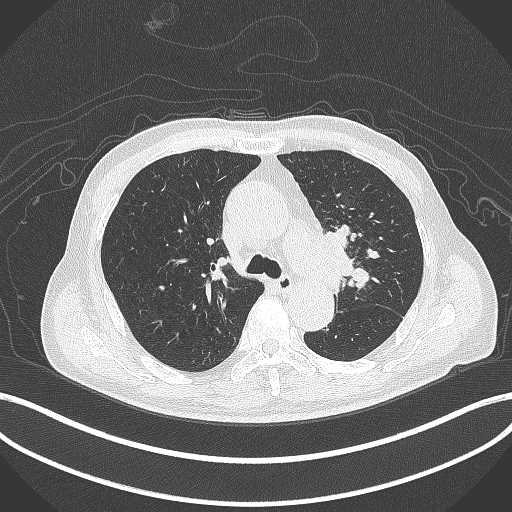
Chest CT, one axial slice; position 291 of 417 along the scan axis; reconstruction kernel B70f; 120 kVp; lung window (W 1500 / L -600 HU); 1 mm slice thickness; 512 × 512 image matrix, field of view 400 × 400 mm. Male patient, age 77 years. Case-level facts recorded for this patient, not image findings: clinical TNM (as recorded): T3 N1 M0.
Annotated regions visible in this slice (bounding box drawn by a radiologist):
- lung tumour (recorded histology: adenocarcinoma): bounding box [x1, y1, x2, y2] px = [313, 227, 354, 289]